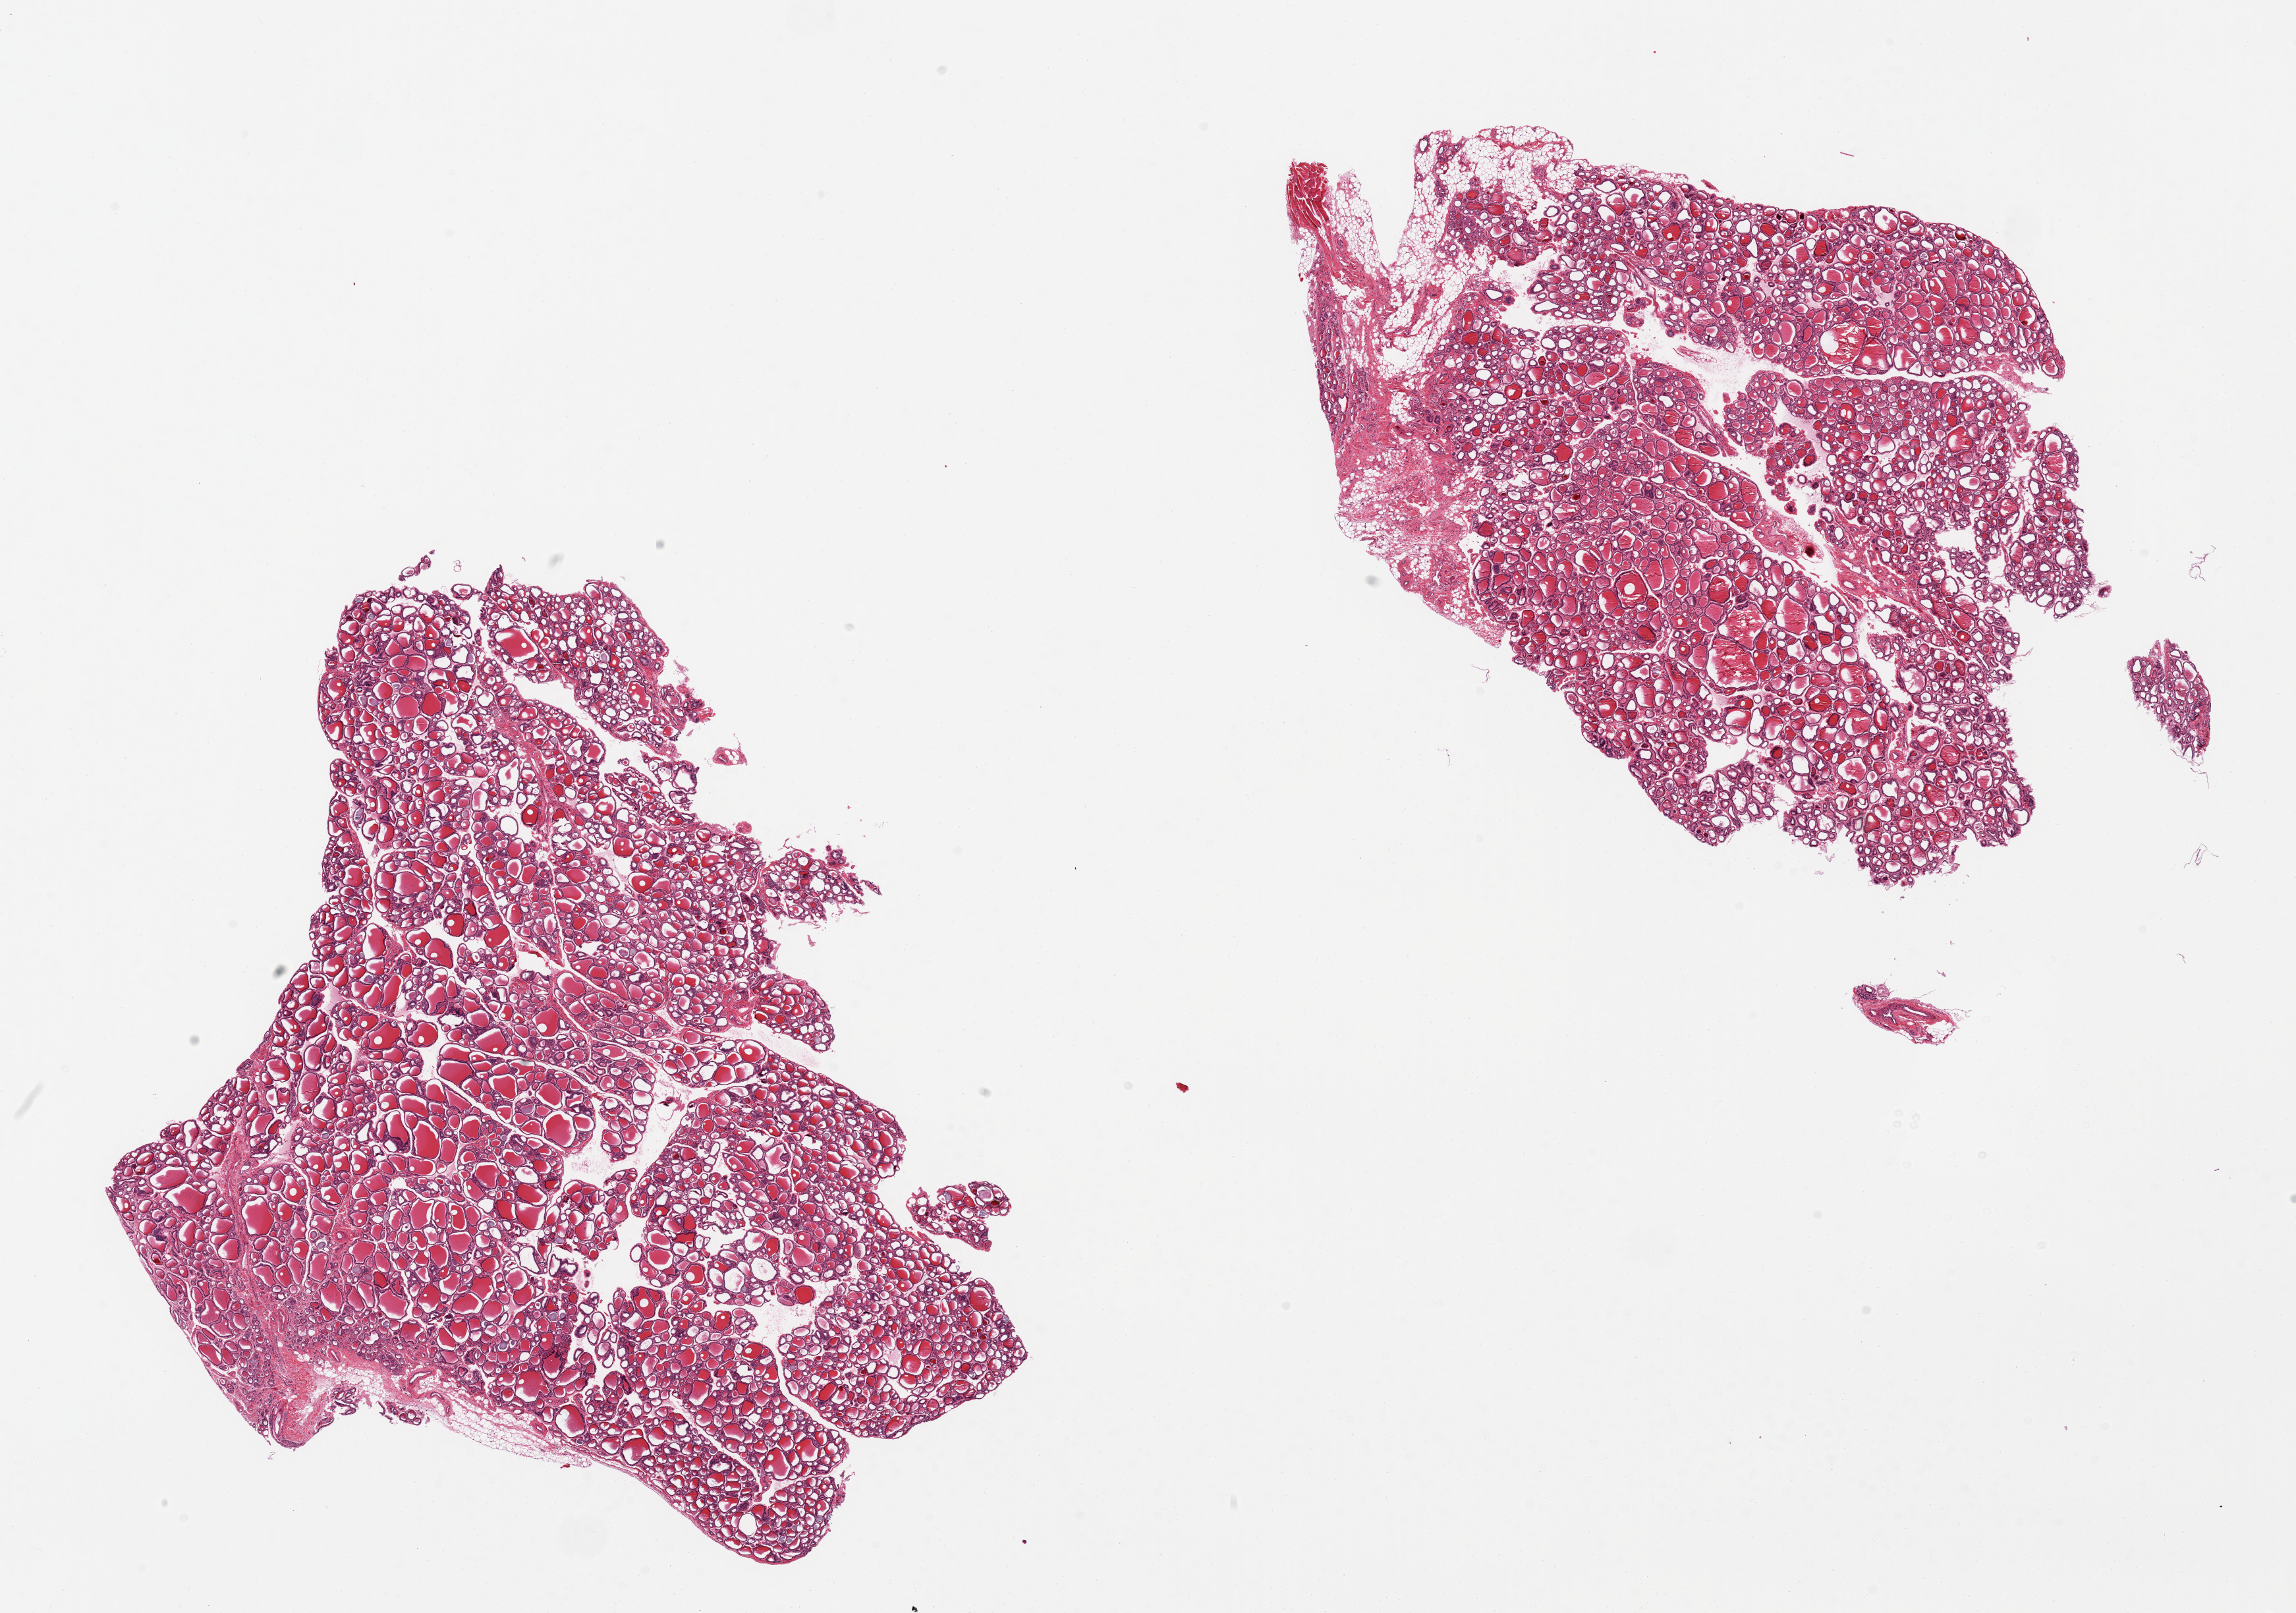
H&E whole-slide image, brightfield, shown as a low-resolution overview of the whole scanned area (about 27.6 x 19.4 mm, from a 20x scan). PAXgene-fixed paraffin-embedded (PFPE) section. Section of thyroid (target tissue). Tissue donor sample. Donor: male.
Reviewer comment on this tissue sample: 2 pieces, small amount of attached fat and skeletal muscle.